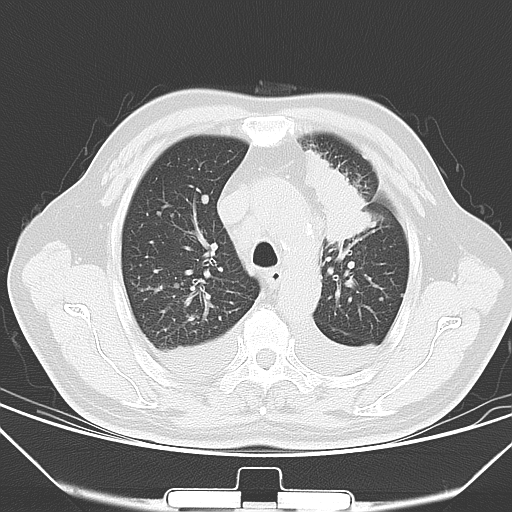
Chest CT, one axial slice; slice 47 of 66 in the series (ordered by position); 120 kVp; lung window (W 1500 / L -600 HU); 5 mm slice thickness; 512 × 512 image matrix. Male patient, age 66 years. From the clinical record (not read from this slice): clinical TNM (as recorded): T1c N0 M0.
Structures marked on this image (bounding box drawn by a radiologist):
- lung tumour (recorded histology: adenocarcinoma): bounding box [x1, y1, x2, y2] px = [298, 146, 378, 240]